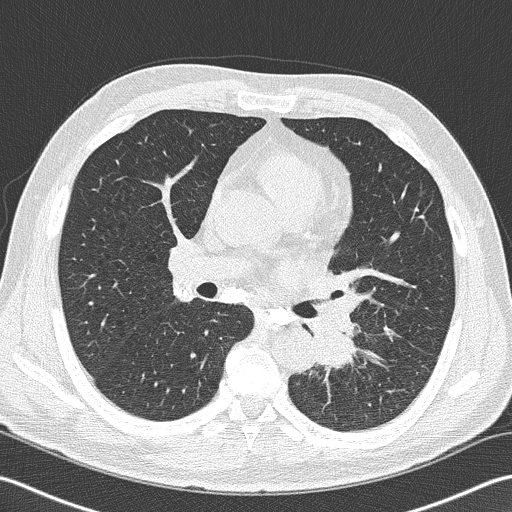
Low-dose screening chest CT, axial slice; second screening round (one year after baseline); lung window (W 1500 / L -600 HU); 2 mm slice thickness; slice 74 of 170 in the series; 512 × 512 image matrix. Male participant, aged 57 years at enrolment. Former smoker at enrolment.
- Expert-annotated lung lesion, box from (x=293, y=302) to (x=373, y=382) px.
- Screening reader's record for this exam (one nodule recorded; not confirmed to be the boxed lesion): non-calcified nodule or mass ≥4 mm, left lower lobe, 40 × 30 mm, spiculated (stellate) margins, soft tissue attenuation, pre-existing on the prior screen: no.
- Official screen result: positive, other.